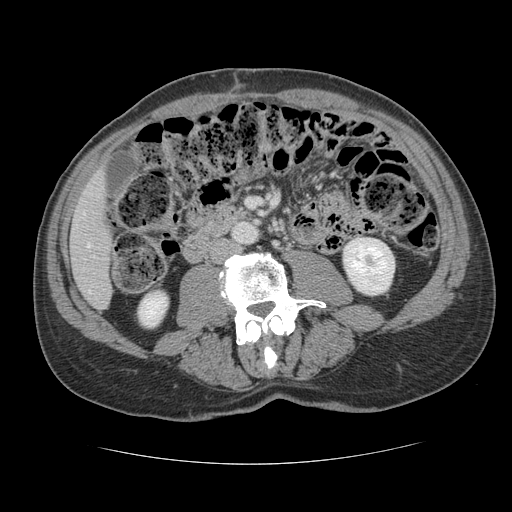
Contrast-enhanced abdominal CT, one axial slice; slice 33 of 134 in the series (ordered by position); reconstruction kernel STANDARD; soft-tissue window (W 400 / L 40 HU); 2.5 mm slice thickness; 512 × 512 image matrix, field of view 377 × 377 mm. Male patient, age 68 years. Case-level facts recorded for this patient, not image findings: diagnosis: colorectal cancer liver metastases, imaged before liver resection; multiple liver metastases: yes; largest metastasis: 2.2 cm.
Annotated regions visible in this slice (manually delineated by an expert):
- hepatic veins: bounding box <87,244,90,247> (left, top, right, bottom; pixels)
- liver: <71,175,112,309>
- planned liver remnant (the part of the liver to remain after resection): <71,175,112,309>